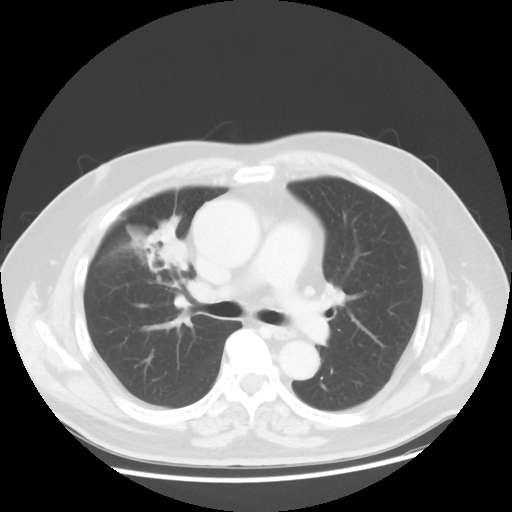
Chest CT, one axial slice. Slice 27 of 48 in the series (ordered by position). 120 kVp. Lung window (W 1500 / L -600 HU). 5 mm slice thickness. 512 × 512 image matrix. Male patient, age 60 years. From the clinical record (not read from this slice): clinical TNM (as recorded): T2 N3 M0; histopathological grade: G2-3.
Annotated regions visible in this slice (rectangle marked by the reading radiologist):
- lung tumour (recorded histology: adenocarcinoma): bounding box (x1, y1, x2, y2) in pixels: (127, 208, 189, 291)